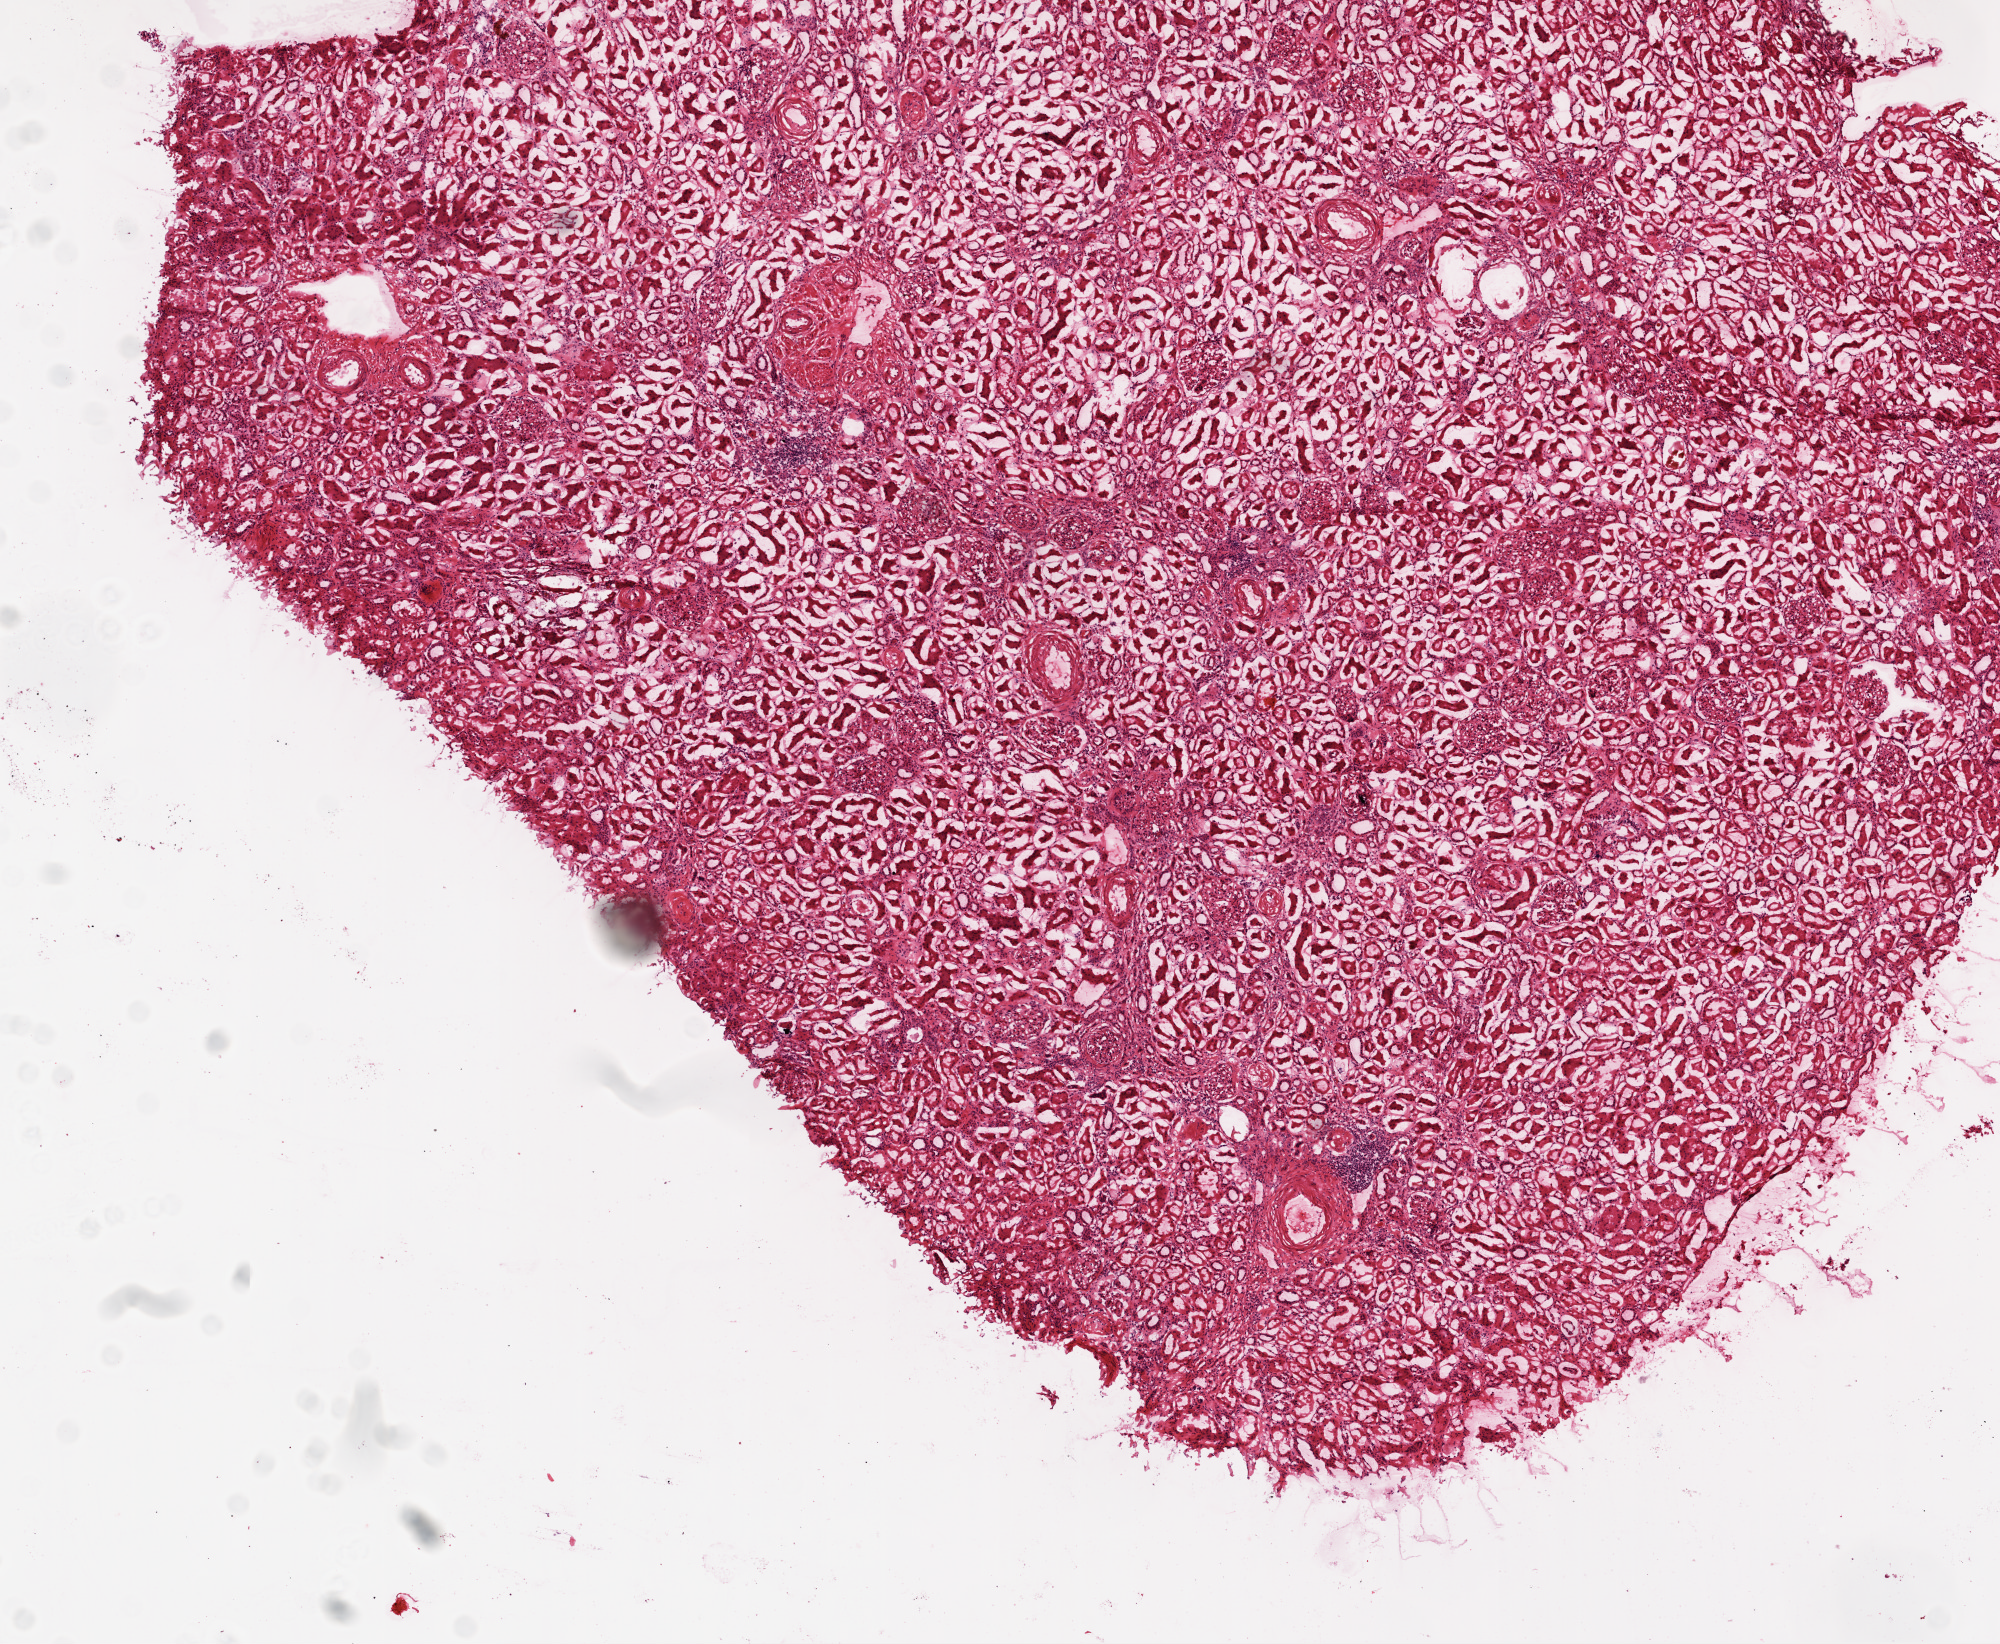
Hematoxylin and eosin (H&E) stained whole-slide image, whole scanned area (about 8.0 x 6.6 mm, from a 20x scan) shown as a low-resolution overview. Frozen section from the top of the tissue portion. Kidney, solid tissue normal (non-tumour tissue) sample. Male patient; age at initial diagnosis 77 years.
This section: solid tissue normal (non-tumour) sample from the same patient. Patient diagnosis: Clear cell adenocarcinoma, NOS.